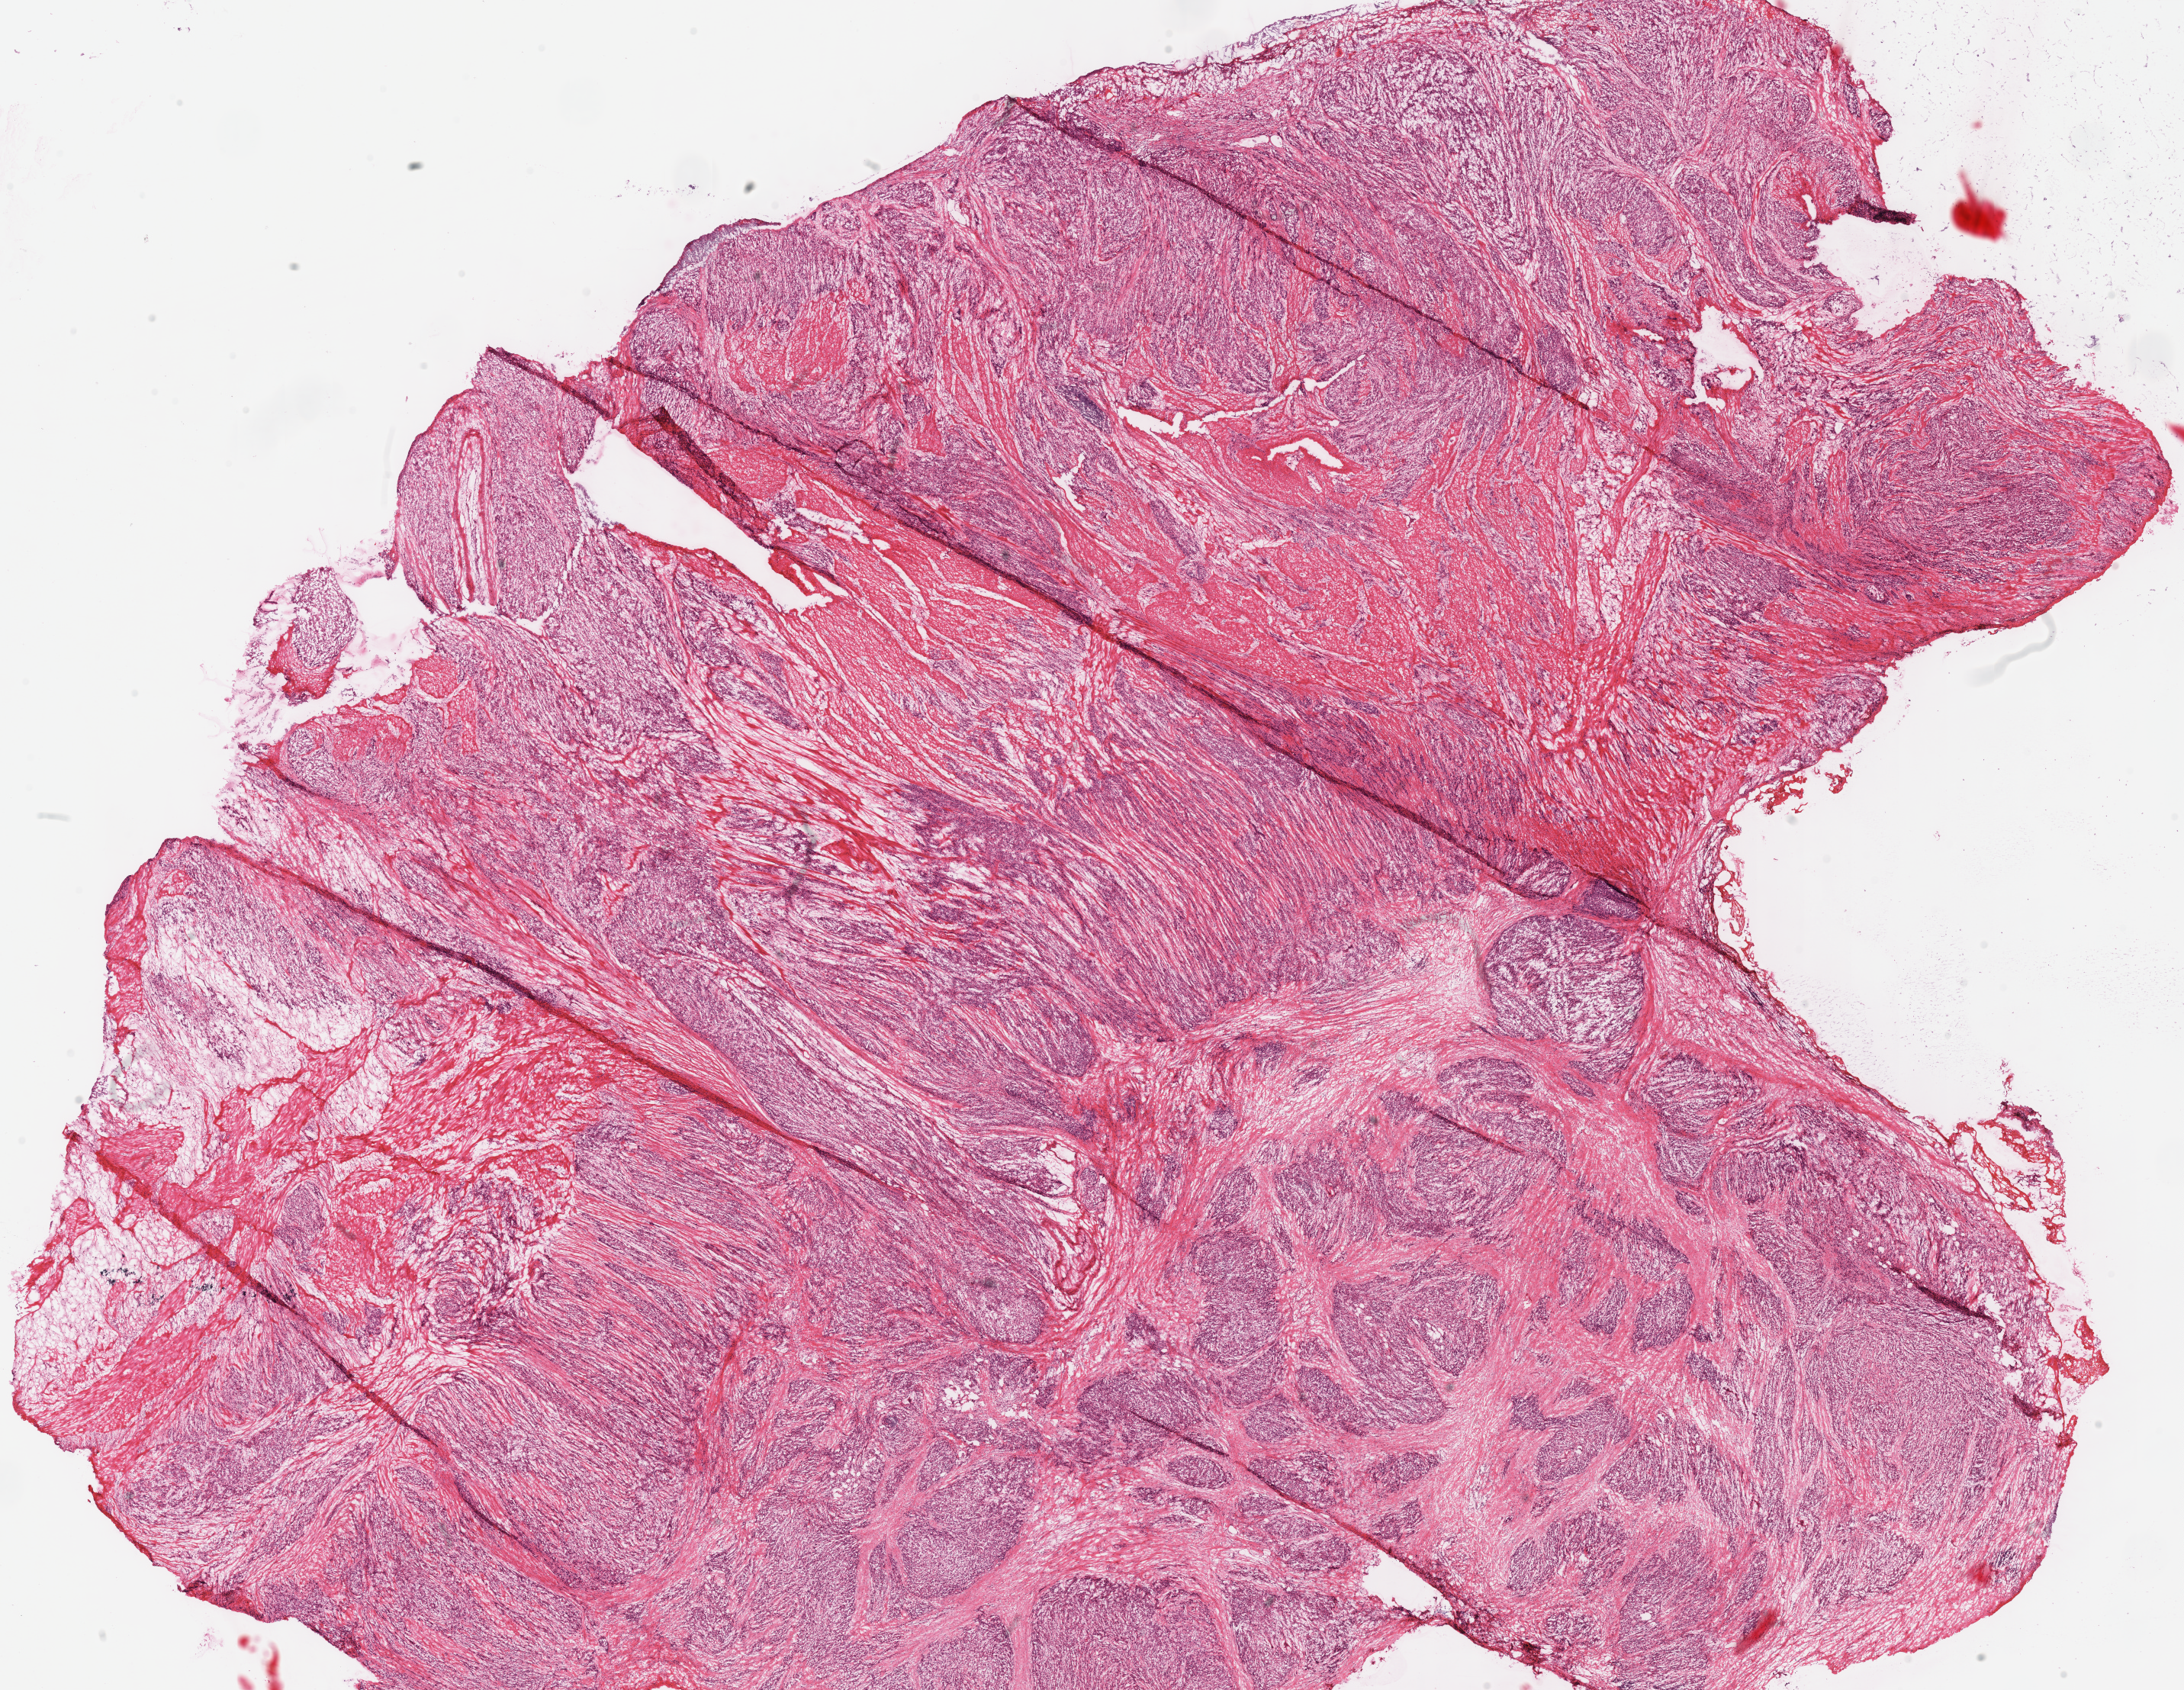
H&E-stained whole-slide image — a low-resolution overview of the entire scanned area, about 22.5 x 17.4 mm, frozen section from the top of the tissue portion, sample: primary tumour, stomach. Male patient; age at initial diagnosis 65 years. Histologic grade: G3 (poorly differentiated). Pathologist review of this section (percent, as recorded): tumour cells 80%, tumour nuclei 70%, normal cells 0%, stromal cells 20%, necrosis 0%.
Lymph nodes positive (case pathology): 15 of 30 examined. Pathologic diagnosis: Adenocarcinoma, NOS (fundus of stomach). AJCC pathologic stage: IIIC. TNM: T4b N3a M0.